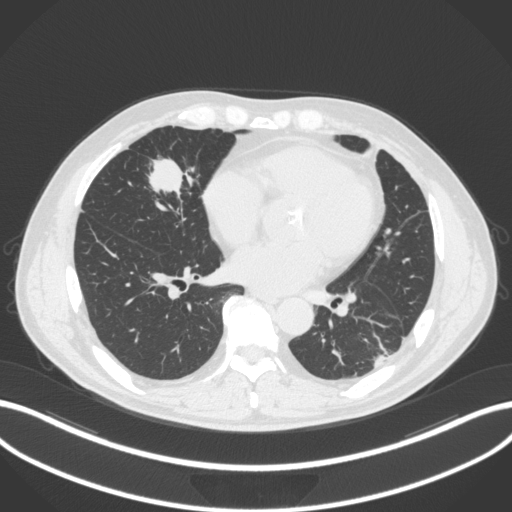
Chest CT, one axial slice. Slice 115 of 399 in the series (ordered by position). Lung window (W 1500 / L -600 HU). 1 mm slice thickness. 512 × 512 image matrix, field of view 400 × 400 mm. Patient: male, 59 years. From the clinical record (not read from this slice): clinical TNM (as recorded): T2a N1 M0.
Structures marked on this image (bounding box drawn by a radiologist):
- lung tumour (recorded histology: adenocarcinoma): box from (x=141, y=150) to (x=196, y=207) px